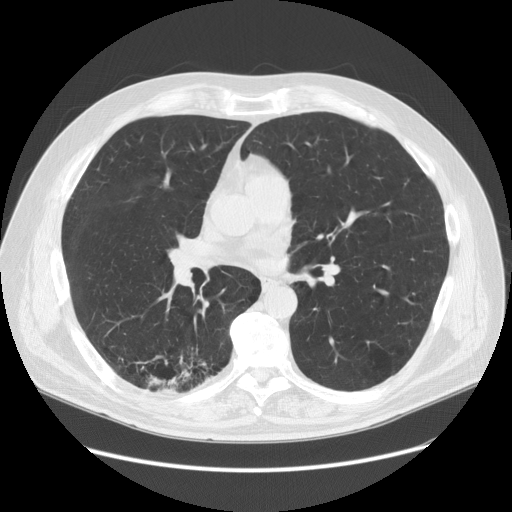
Low-dose screening chest CT, one axial slice. Slice 76 of 149 in the series (ordered by position). Reconstruction kernel STANDARD. 120 kVp. Lung window (W 1500 / L -600 HU). 2.5 mm slice thickness. 512 × 512 image matrix.
Structures marked on this image (outlined manually by an expert reader):
- lesion 1 (tumor, lower lobe of right lung): bounding box <145,369,192,394> (left, top, right, bottom; pixels)